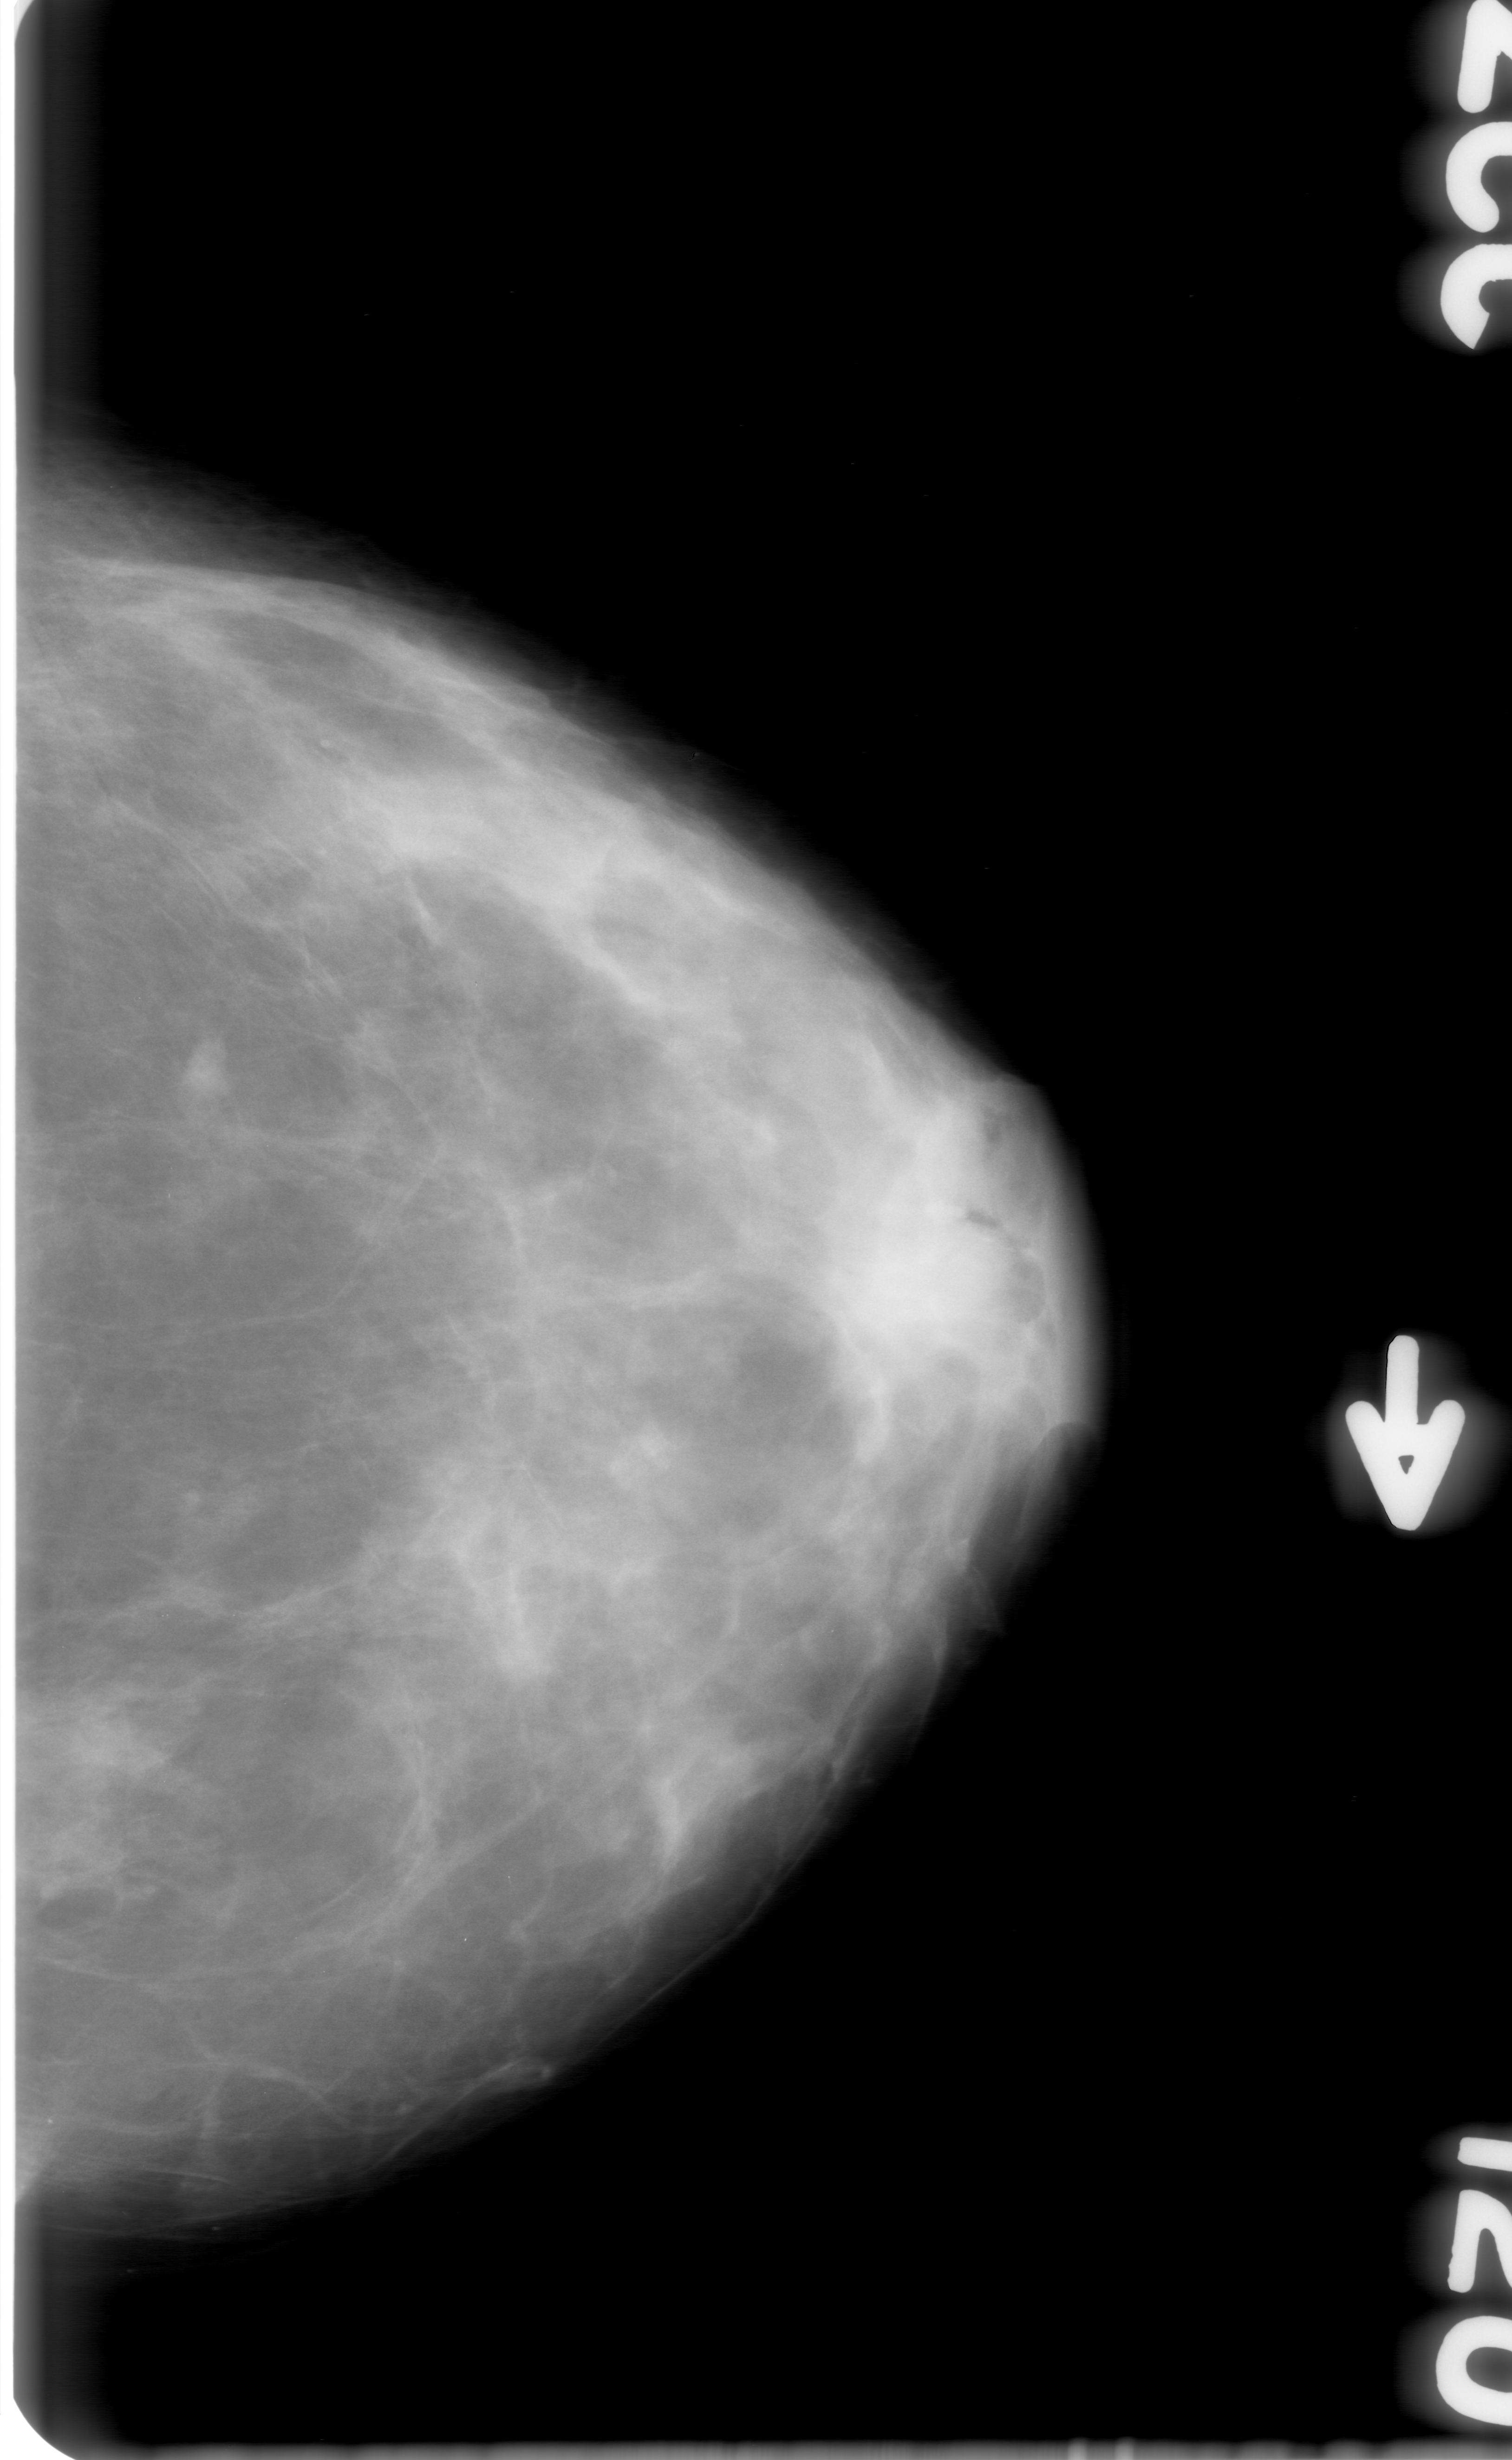
Mammogram (digitized film); left breast; craniocaudal (CC) view; BI-RADS breast density category 3 (scale 1–4).
- Marked findings (only marked abnormalities are described; nothing is implied about the rest of the image): mass, shape irregular, margins obscured; BI-RADS assessment category 0 (incomplete: needs additional imaging); subtlety rating 3 on a 1 (subtle) to 5 (obvious) scale; pathology (as recorded): benign.